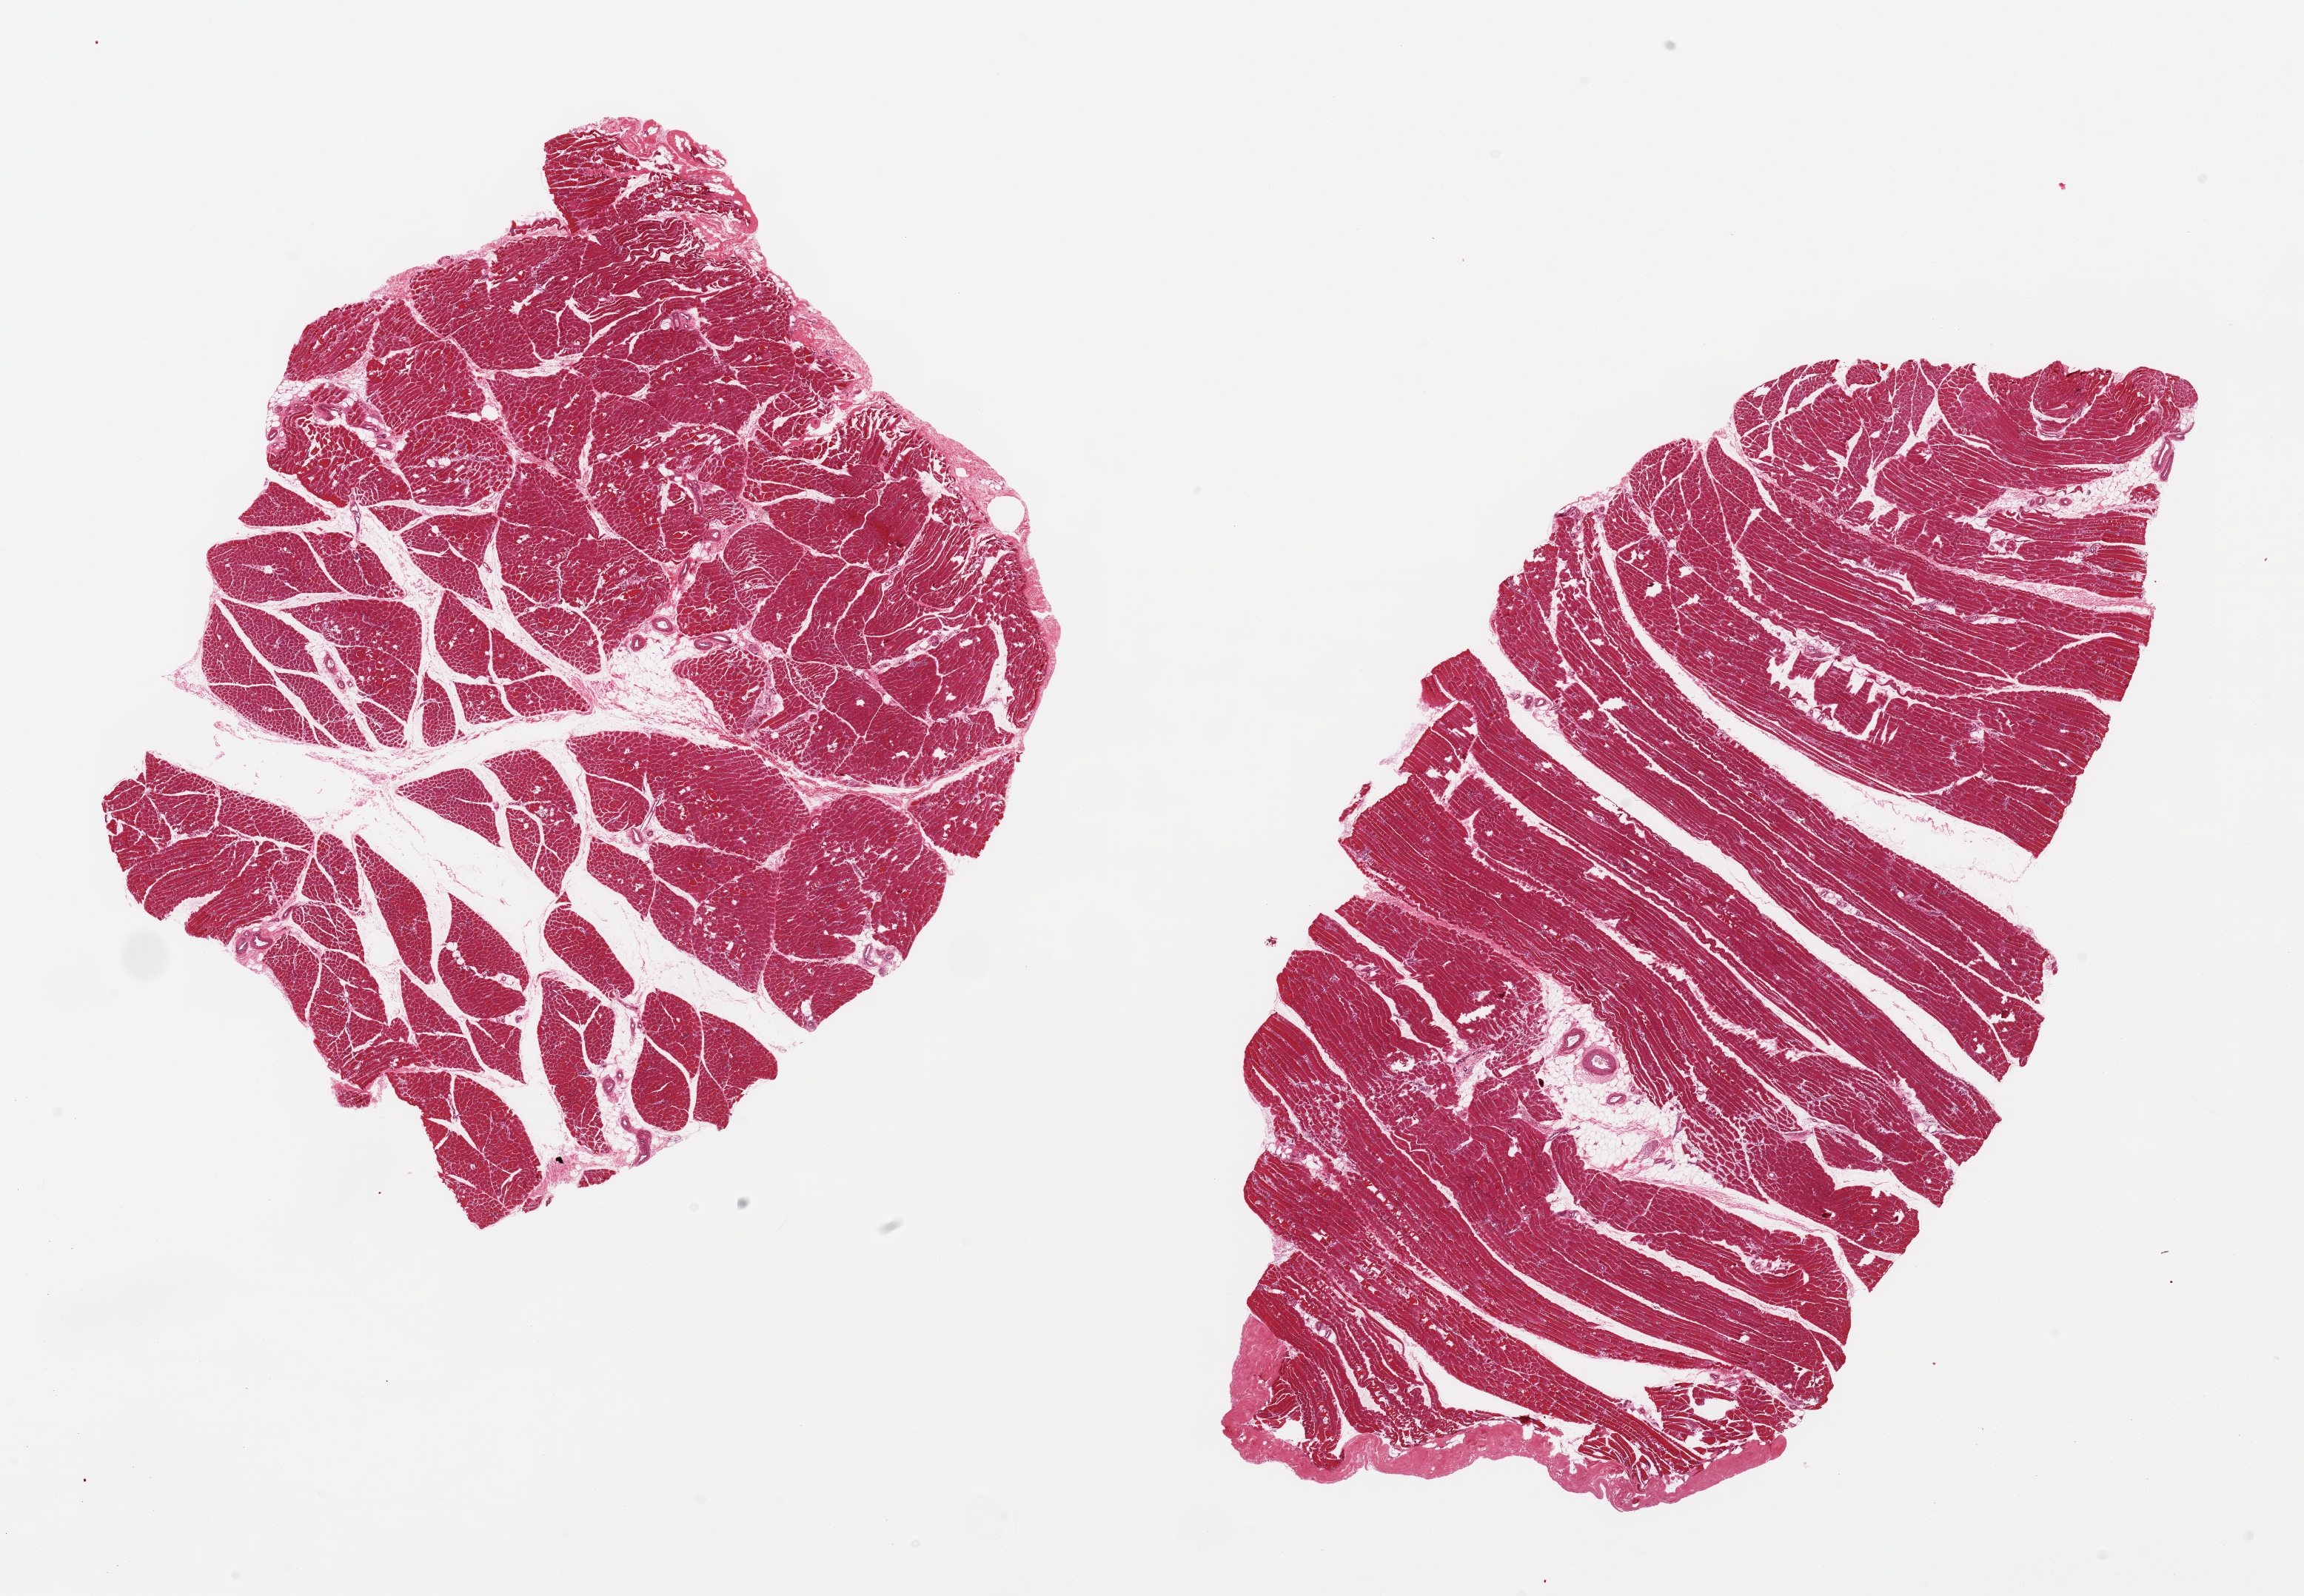
H&E whole-slide image — whole scanned area (about 24.6 x 17.1 mm) shown as a low-resolution overview, PAXgene-fixed, paraffin-embedded tissue, target tissue: skeletal muscle, tissue donor sample. Donor: male.
• review note (as recorded): 2 ~11x7mm pieces, ~10-20% intermingled fat